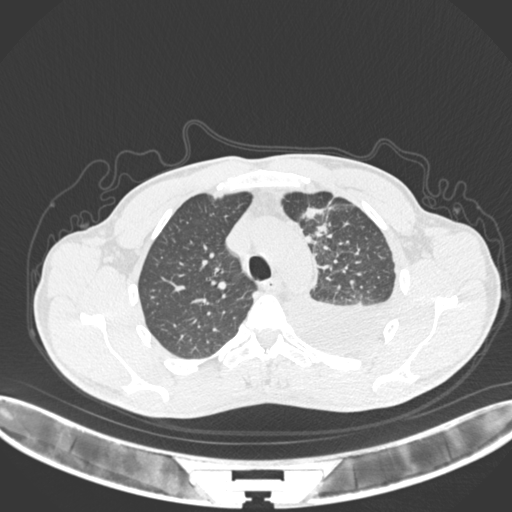
Chest CT, one axial slice; 120 kVp; lung window (W 1500 / L -600 HU); 512 × 512 image matrix, field of view 400 × 400 mm. Patient: male, 49 years. From the clinical record (not read from this slice): clinical TNM (as recorded): T1c N1 M1.
Outlined on this slice (rectangle marked by the reading radiologist):
- lung tumour (recorded histology: adenocarcinoma): bounding box <299,206,336,224> (left, top, right, bottom; pixels)